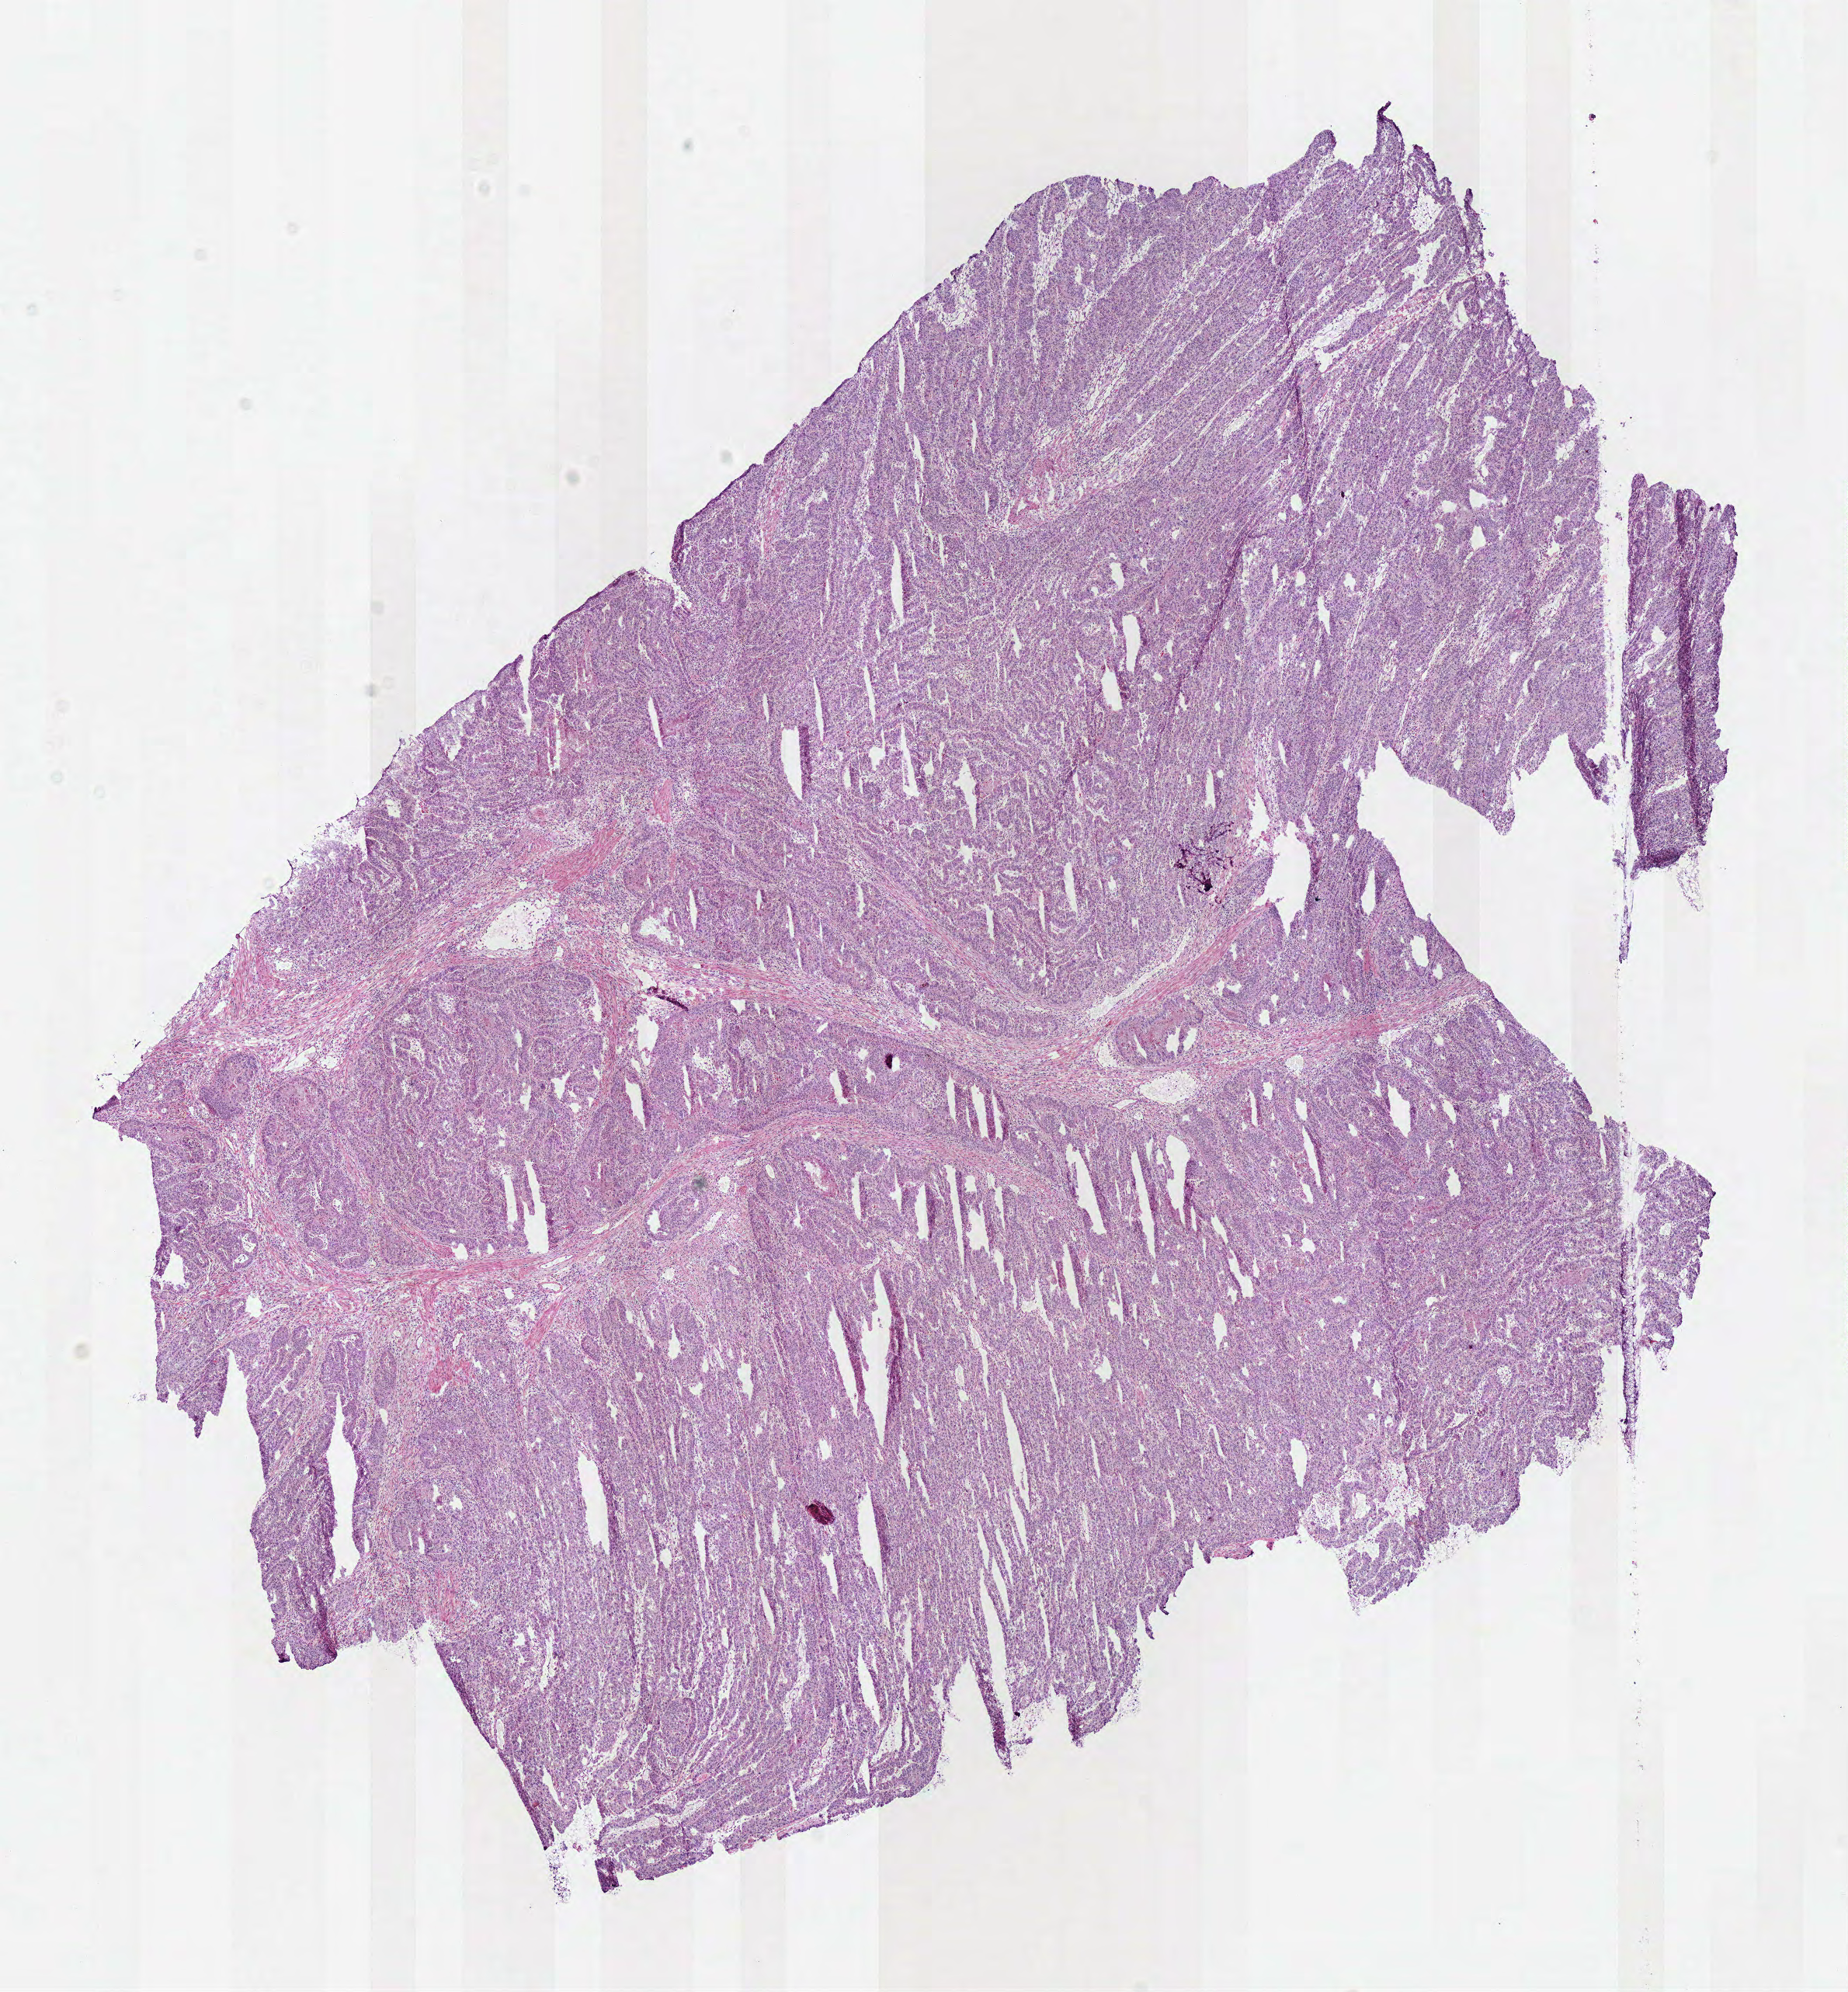
Digitized H&E tissue section (whole slide) — whole scanned area (about 9.4 x 10.1 mm) shown as a low-resolution overview; frozen section from the bottom of the tissue portion; primary tumour sample from the stomach. Male patient; age at initial diagnosis 77 years. Histologic grade: G2 (moderately differentiated). Pathologist review of this section (percent, as recorded): tumour cells 87%, tumour nuclei 75%, normal cells 0%, stromal cells 8%, necrosis 5%.
AJCC pathologic stage: IB. Lymph nodes positive (case pathology): 0 of 7 examined. TNM: T2 N0 M0. Pathologic diagnosis: Tubular adenocarcinoma.